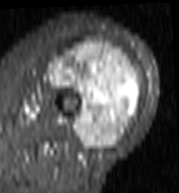
MRI of an extremity soft-tissue mass, one axial slice; position 53 of 103 along the scan axis; STIR; MR volume resampled by the dataset authors to the PET/CT grid (not the native acquisition matrix); 3.27 mm slice thickness; 179 × 193 image matrix, field of view 175 × 188 mm. Female patient. Case-level facts recorded for this patient, not image findings: histological type: undifferentiated – high grade; grade: high; site of the primary tumour: left thigh.
Outlined on this slice (expert contour drawn on MRI and transferred to this co-registered scan by the dataset authors):
- gross tumour volume including surrounding oedema: bounding box <47,39,142,150> (left, top, right, bottom; pixels)
- gross tumour volume (mass): <48,39,140,150>